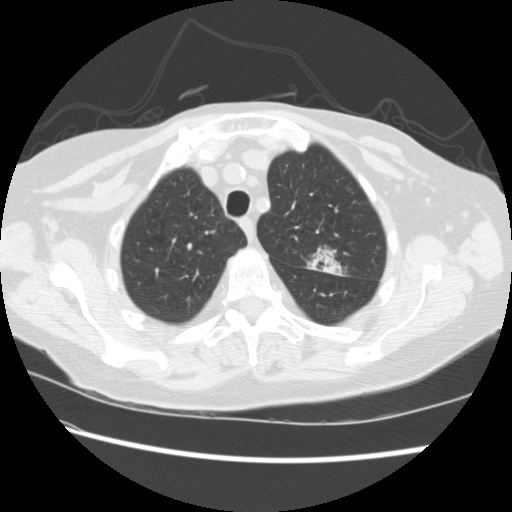
Axial slice from a low-dose chest CT screening exam; baseline screening round; lung window (W 1500 / L -600 HU); 120 kVp; slice 49 of 224 in the series; 512 × 512 image matrix. Female participant, aged 74 years at enrolment. Former smoker at enrolment.
Expert-annotated lung lesion, box from (x=297, y=240) to (x=347, y=281) px. The screening reader recorded 2 non-calcified nodules or masses ≥4 mm on this exam (left upper lobe, right lower lobe); which of them this box marks is not recorded. Official screen result: positive, change unspecified: nodule(s) >= 4 mm or enlarging nodule(s), mass(es), or other non-specific abnormalities suspicious for lung cancer. Participant outcome: lung cancer diagnosed 309 days after this screen — non-small cell carcinoma, left upper lobe, stage IV (AJCC 6th edition).